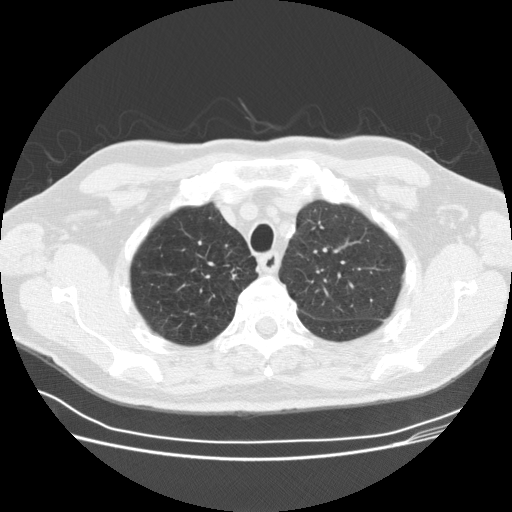
Low-dose screening chest CT, one axial slice; slice 130 of 164 in the series (ordered by position); 120 kVp; lung window (W 1500 / L -600 HU); 512 × 512 image matrix, field of view 360 × 360 mm.
Annotated regions visible in this slice (manually delineated by an expert):
- lesion 1 (tumor, upper lobe of right lung): bounding box [x1, y1, x2, y2] px = [229, 267, 242, 281]